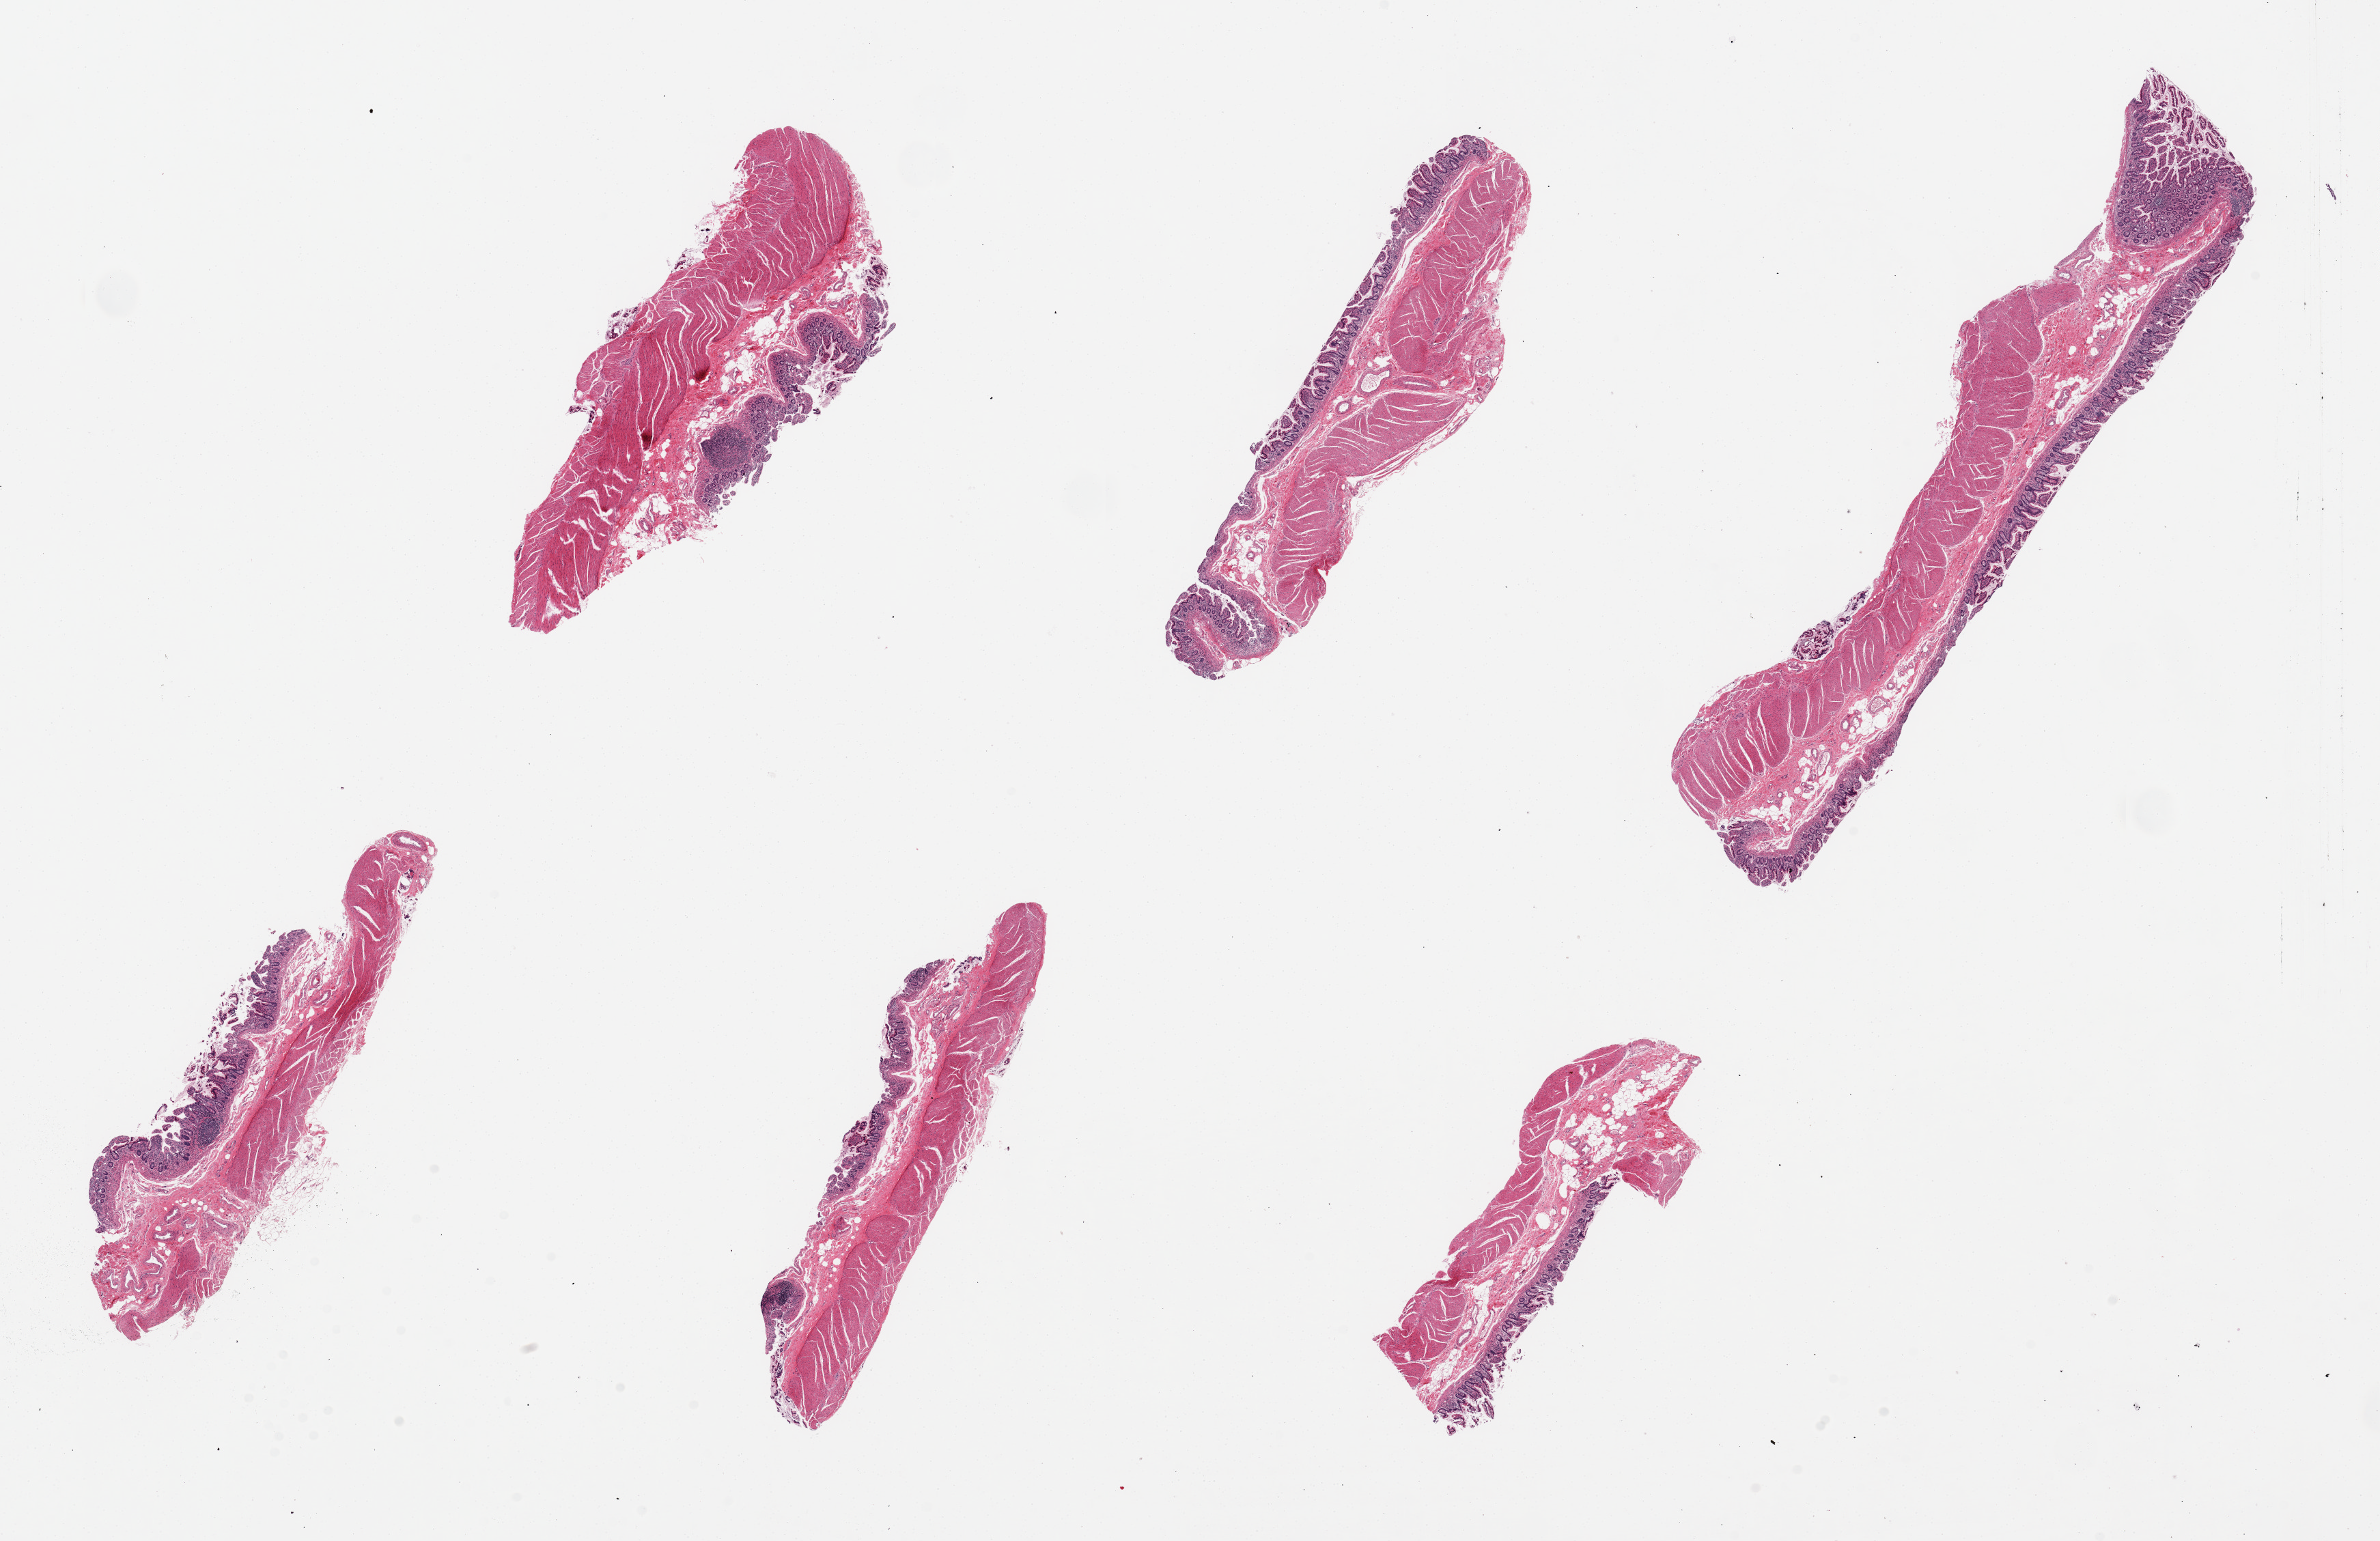
Whole-slide image, H&E stain, brightfield, shown as a low-resolution overview of the whole scanned area (about 27.6 x 17.9 mm, acquisition: 20x scan). PAXgene-fixed, paraffin-embedded tissue. Section of ileum (target tissue). Tissue donor sample.
Pathologist's review note for this sample: 6 pieces, up to 10x2mm; Several small lymphoid nodules; All pieces have muscularis propria.